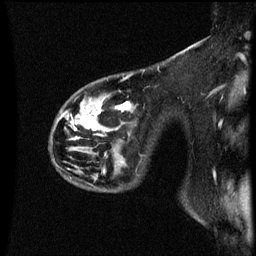
Breast MRI (dynamic contrast-enhanced), one sagittal slice. Dynamic contrast-enhanced series, image 2 of 3 at this slice position (ordered by acquisition). 1.5 T. TE 4.2 ms, TR 8.9 ms. 2 mm slice thickness. 256 × 256 image matrix, field of view 200 × 200 mm. Patient: female, 44 years. Case-level facts recorded for this patient, not image findings: setting: breast cancer imaged before/during neoadjuvant chemotherapy; receptor status: HR-positive, HER2-negative.
Annotated regions visible in this slice (semi-automatically segmented with operator editing):
- analysis volume of interest (the breast-tissue region the enhancement analysis was run in; not a lesion): box from (x=50, y=78) to (x=137, y=187) px
- tumour enhancement mask (voxels above the 70 % enhancement threshold inside the analysis volume of interest): (x=85, y=102)–(x=130, y=131)